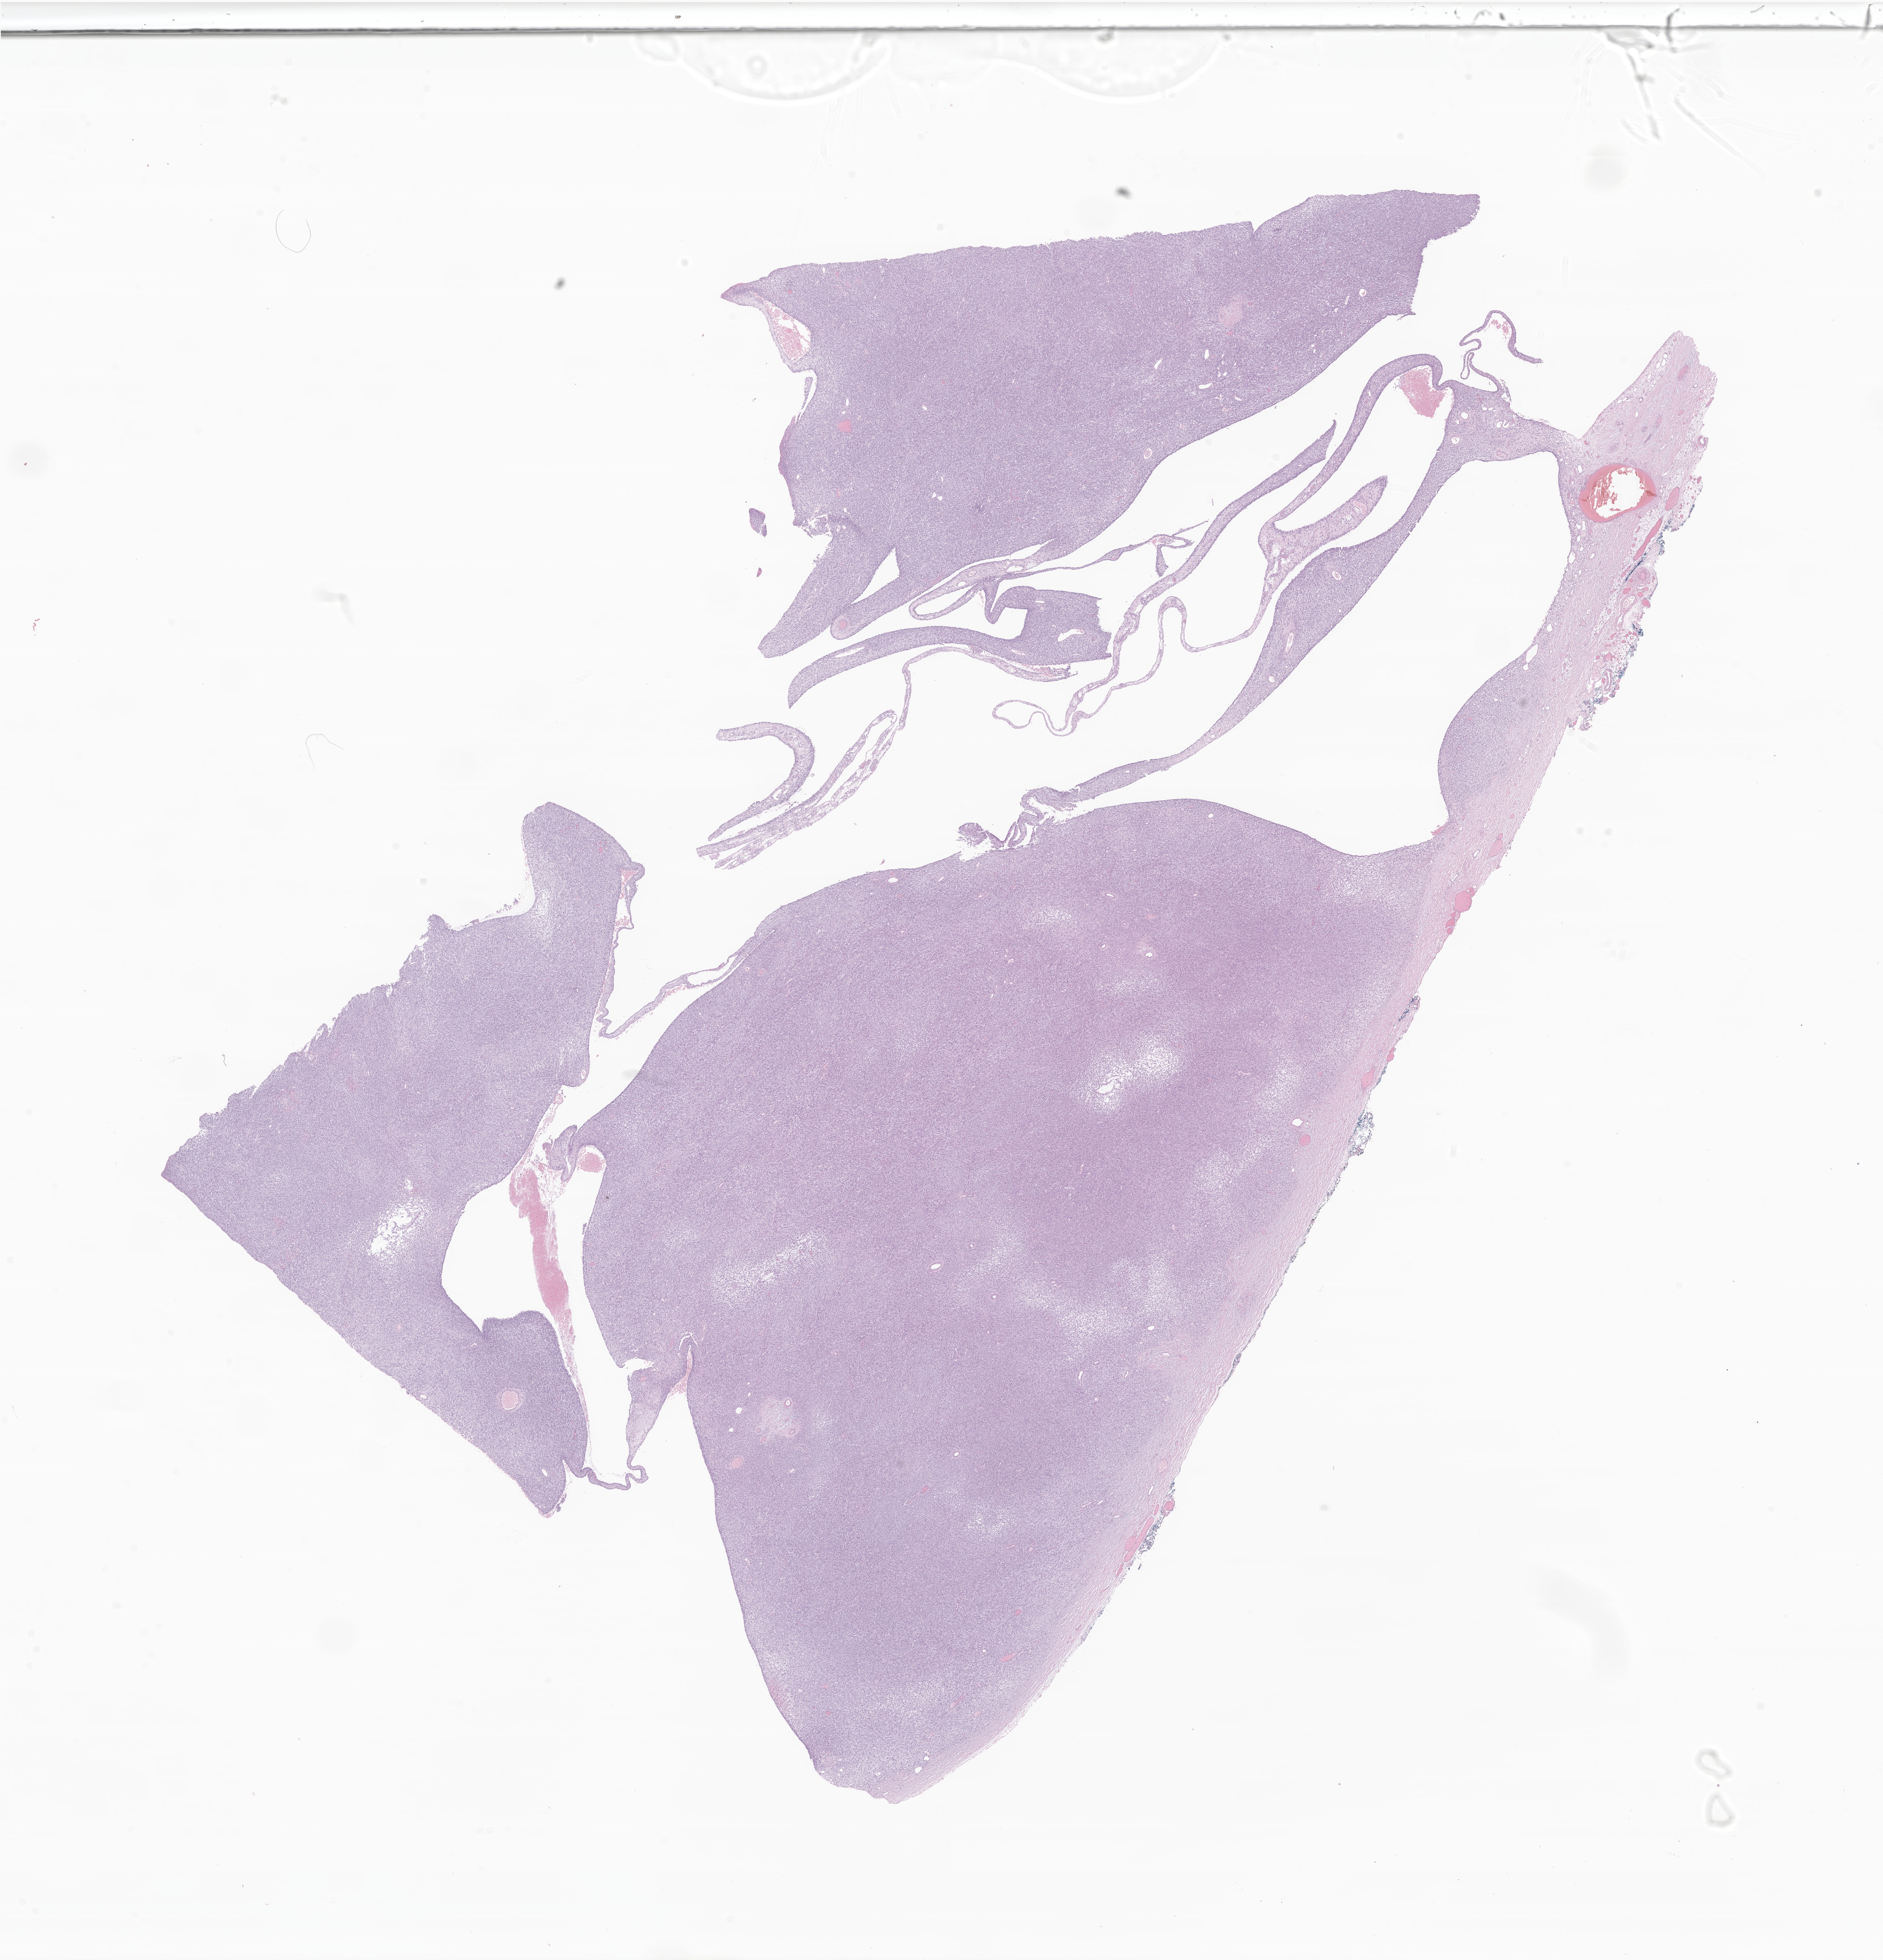
Digitized H&E-stained section of tumor tissue from the retroperitoneum, shown as a low-resolution overview of the whole scanned area (about 22.3 x 23.2 mm), formalin-fixed paraffin-embedded section. Patient male; age 642 days (about 1.8 years).
Diagnosis (ICD-O-3 morphology term): Sarcoma, NOS.